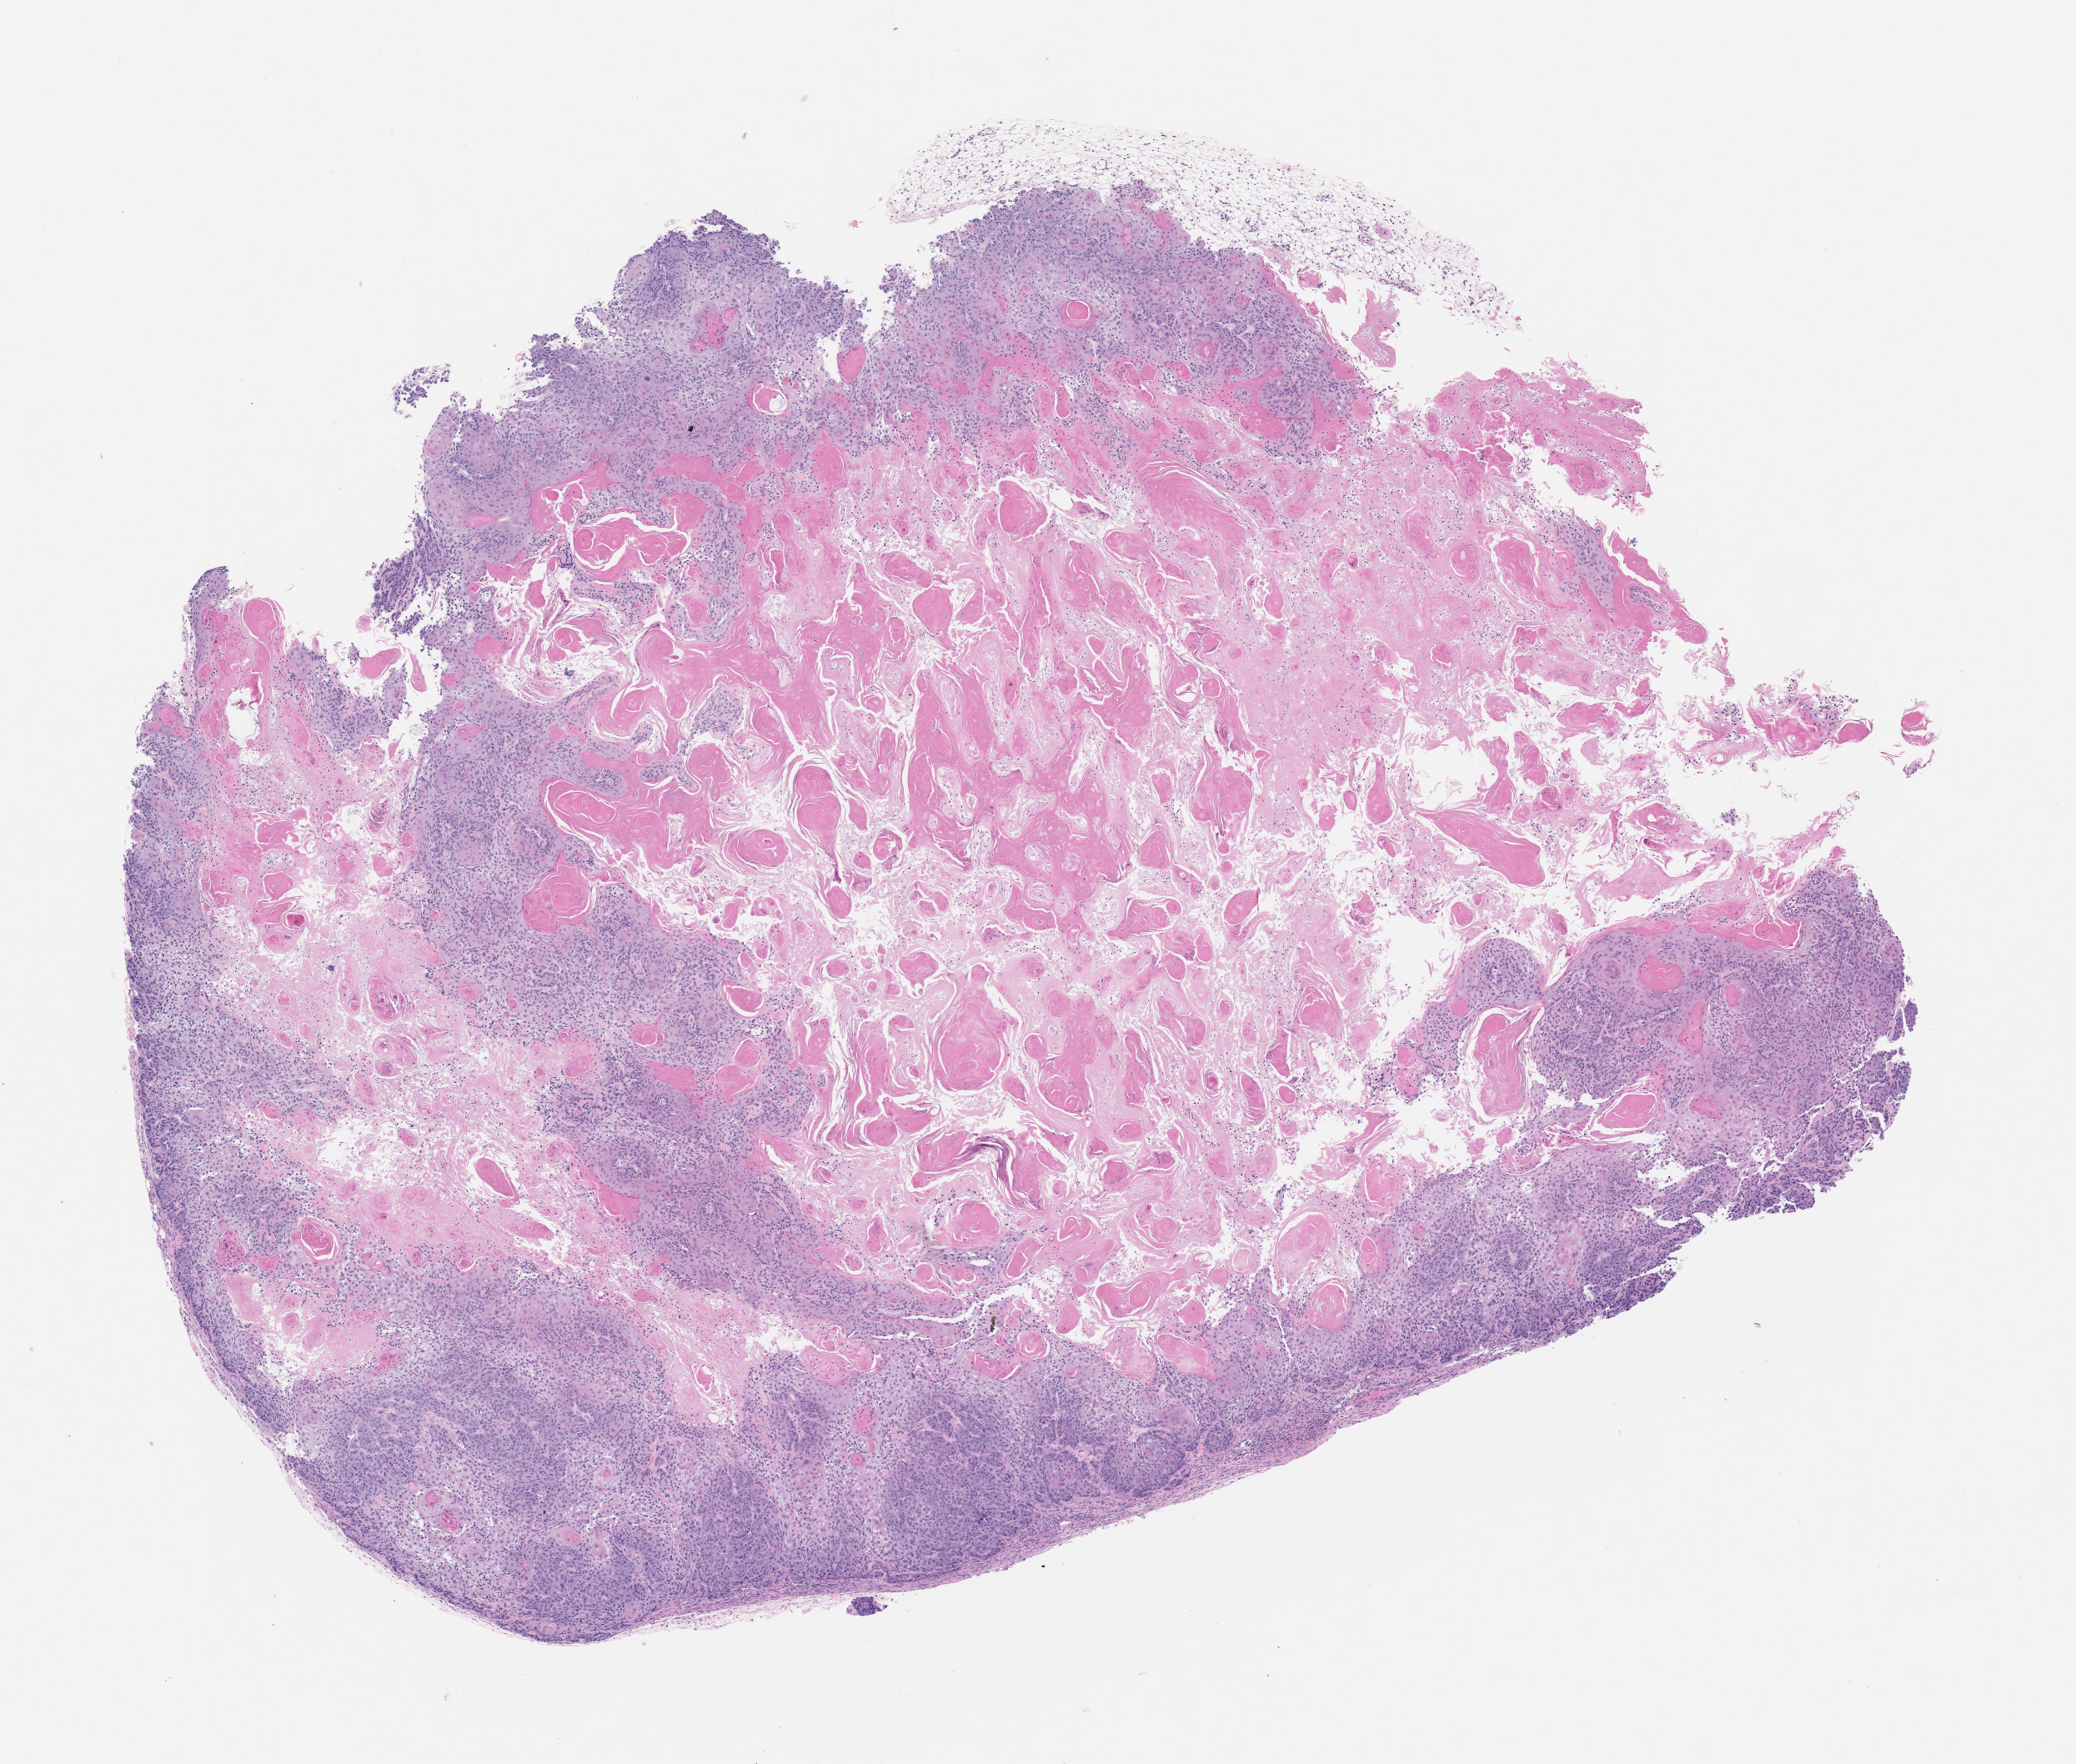
Whole-slide image, haematoxylin and eosin: patient-derived xenograft (human tumor grown in a mouse), passage 2, a low-resolution overview of the entire scanned area, about 10.0 x 8.5 mm; formalin-fixed paraffin-embedded section; originating tumor site category: oral soft tissue.
Originating patient diagnosis: Head and Neck Squamous Cell Carcinoma.